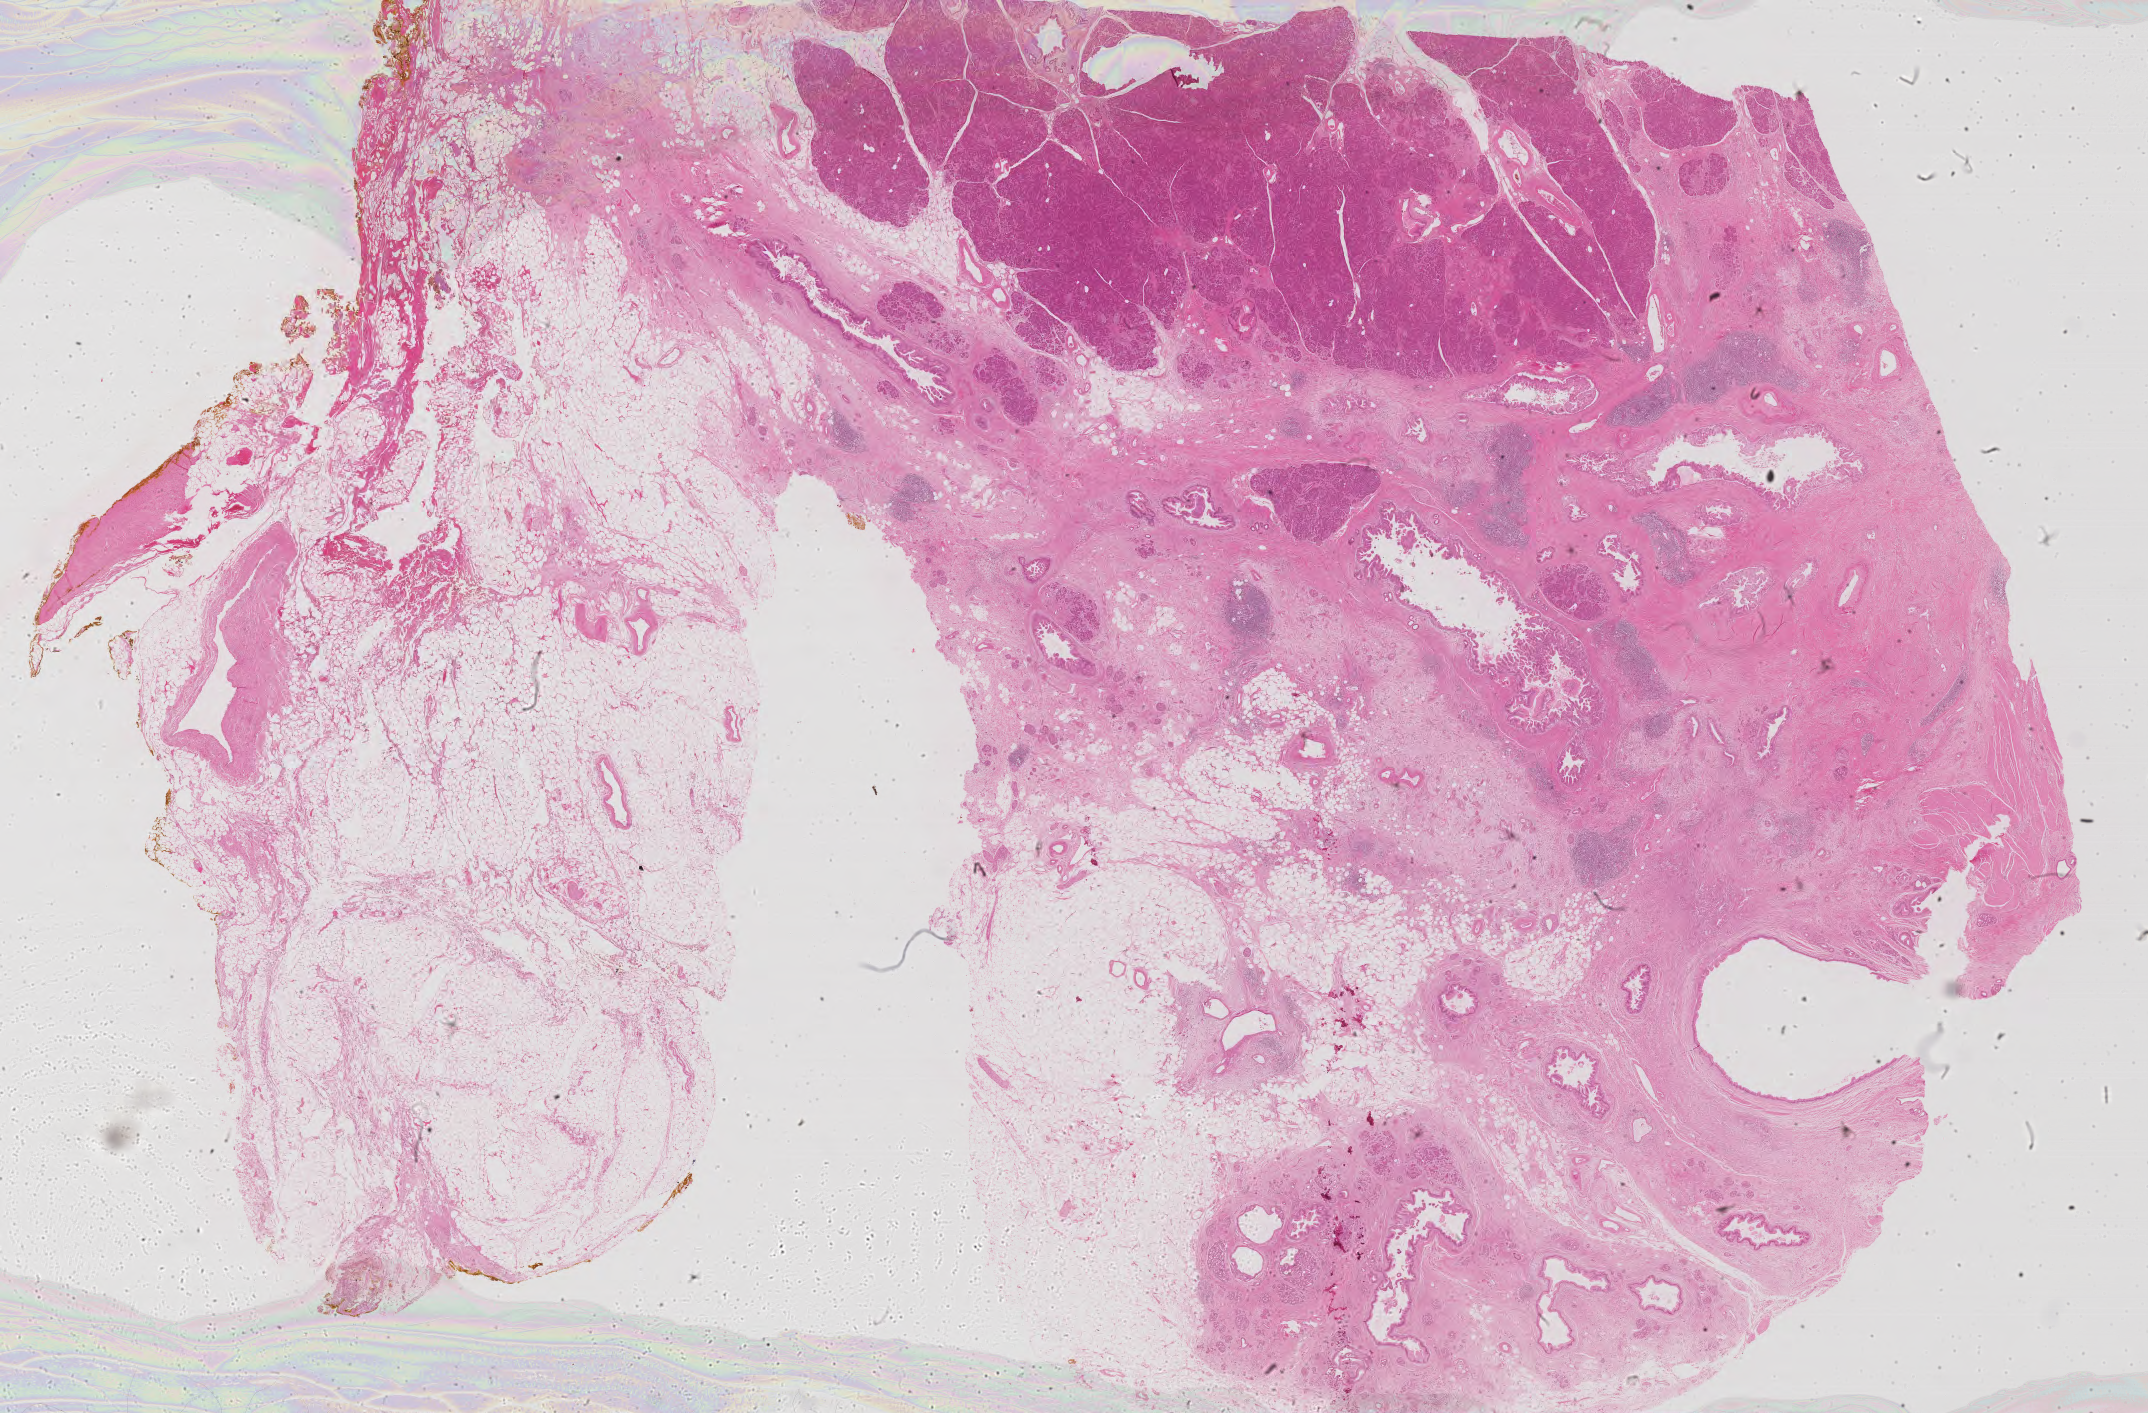
Digitized H&E tissue section (whole slide) — low-resolution overview of the scanned area, about 34.4 x 22.6 mm (from a 40x scan); FFPE section; primary tumour sample from the pancreas. Patient: male, age at initial diagnosis 71 years.
Histologic diagnosis: Infiltrating duct carcinoma, NOS (head of pancreas).